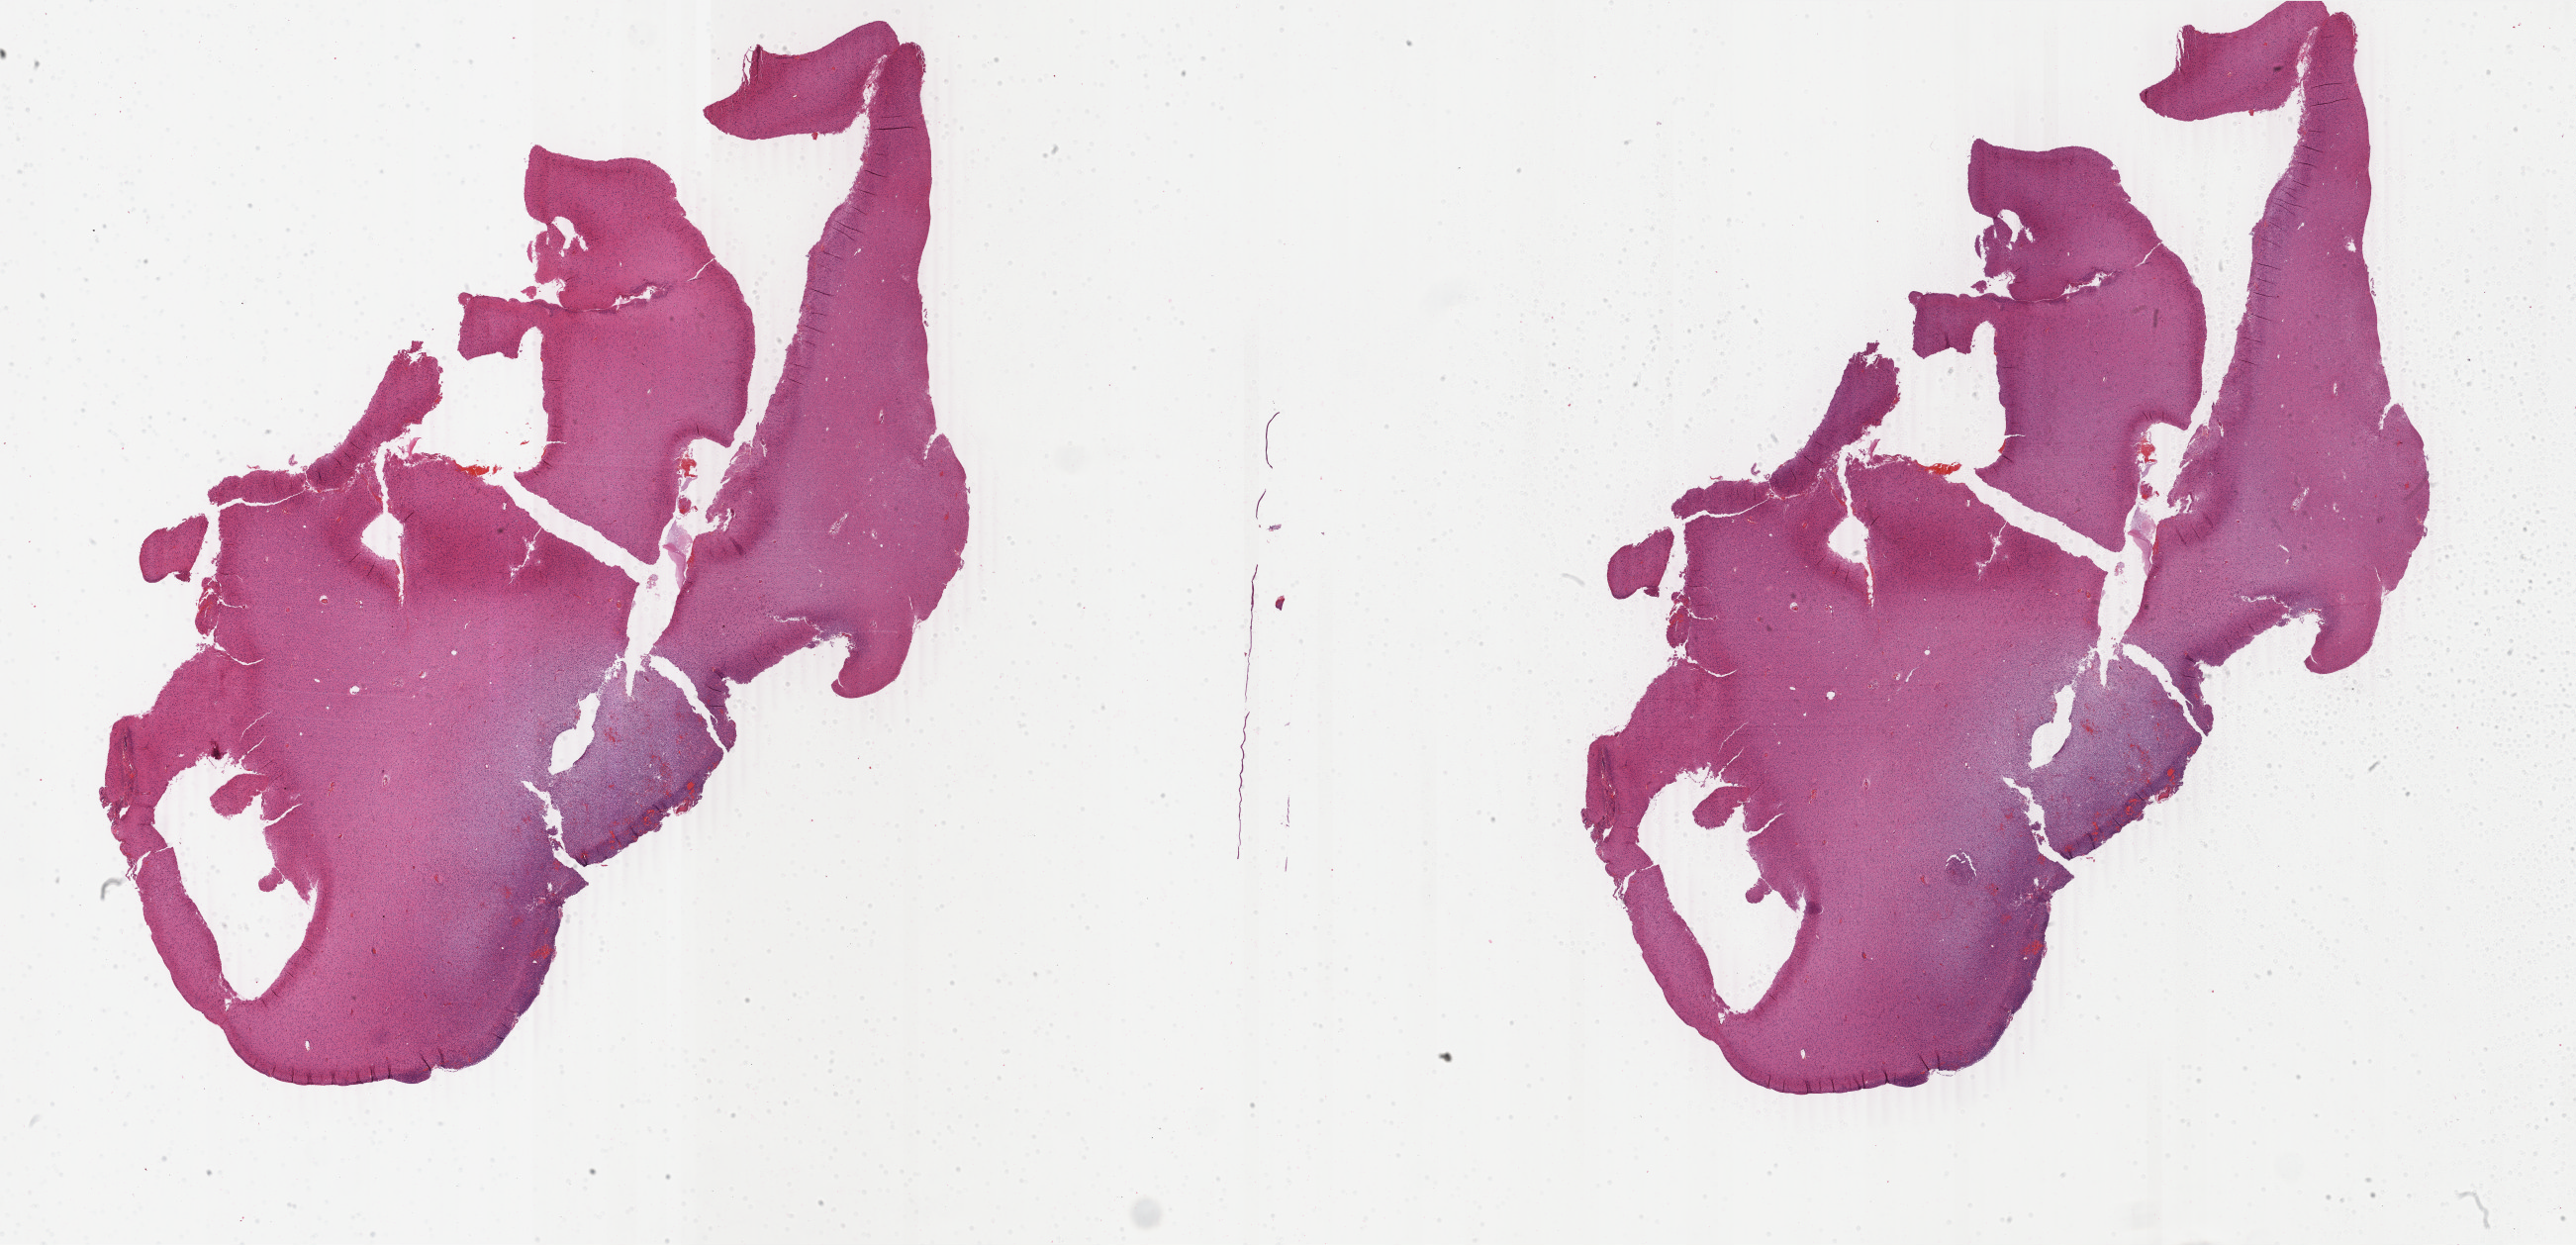
H&E-stained whole-slide image, whole scanned area (about 41.4 x 20.0 mm) shown as a low-resolution overview. Formalin-fixed paraffin-embedded (FFPE) diagnostic section. Primary tumour sample from the brain. Female, age 49 years at initial diagnosis. Histologic grade: G3 (poorly differentiated).
Histologic diagnosis: Oligodendroglioma, anaplastic (cerebrum).